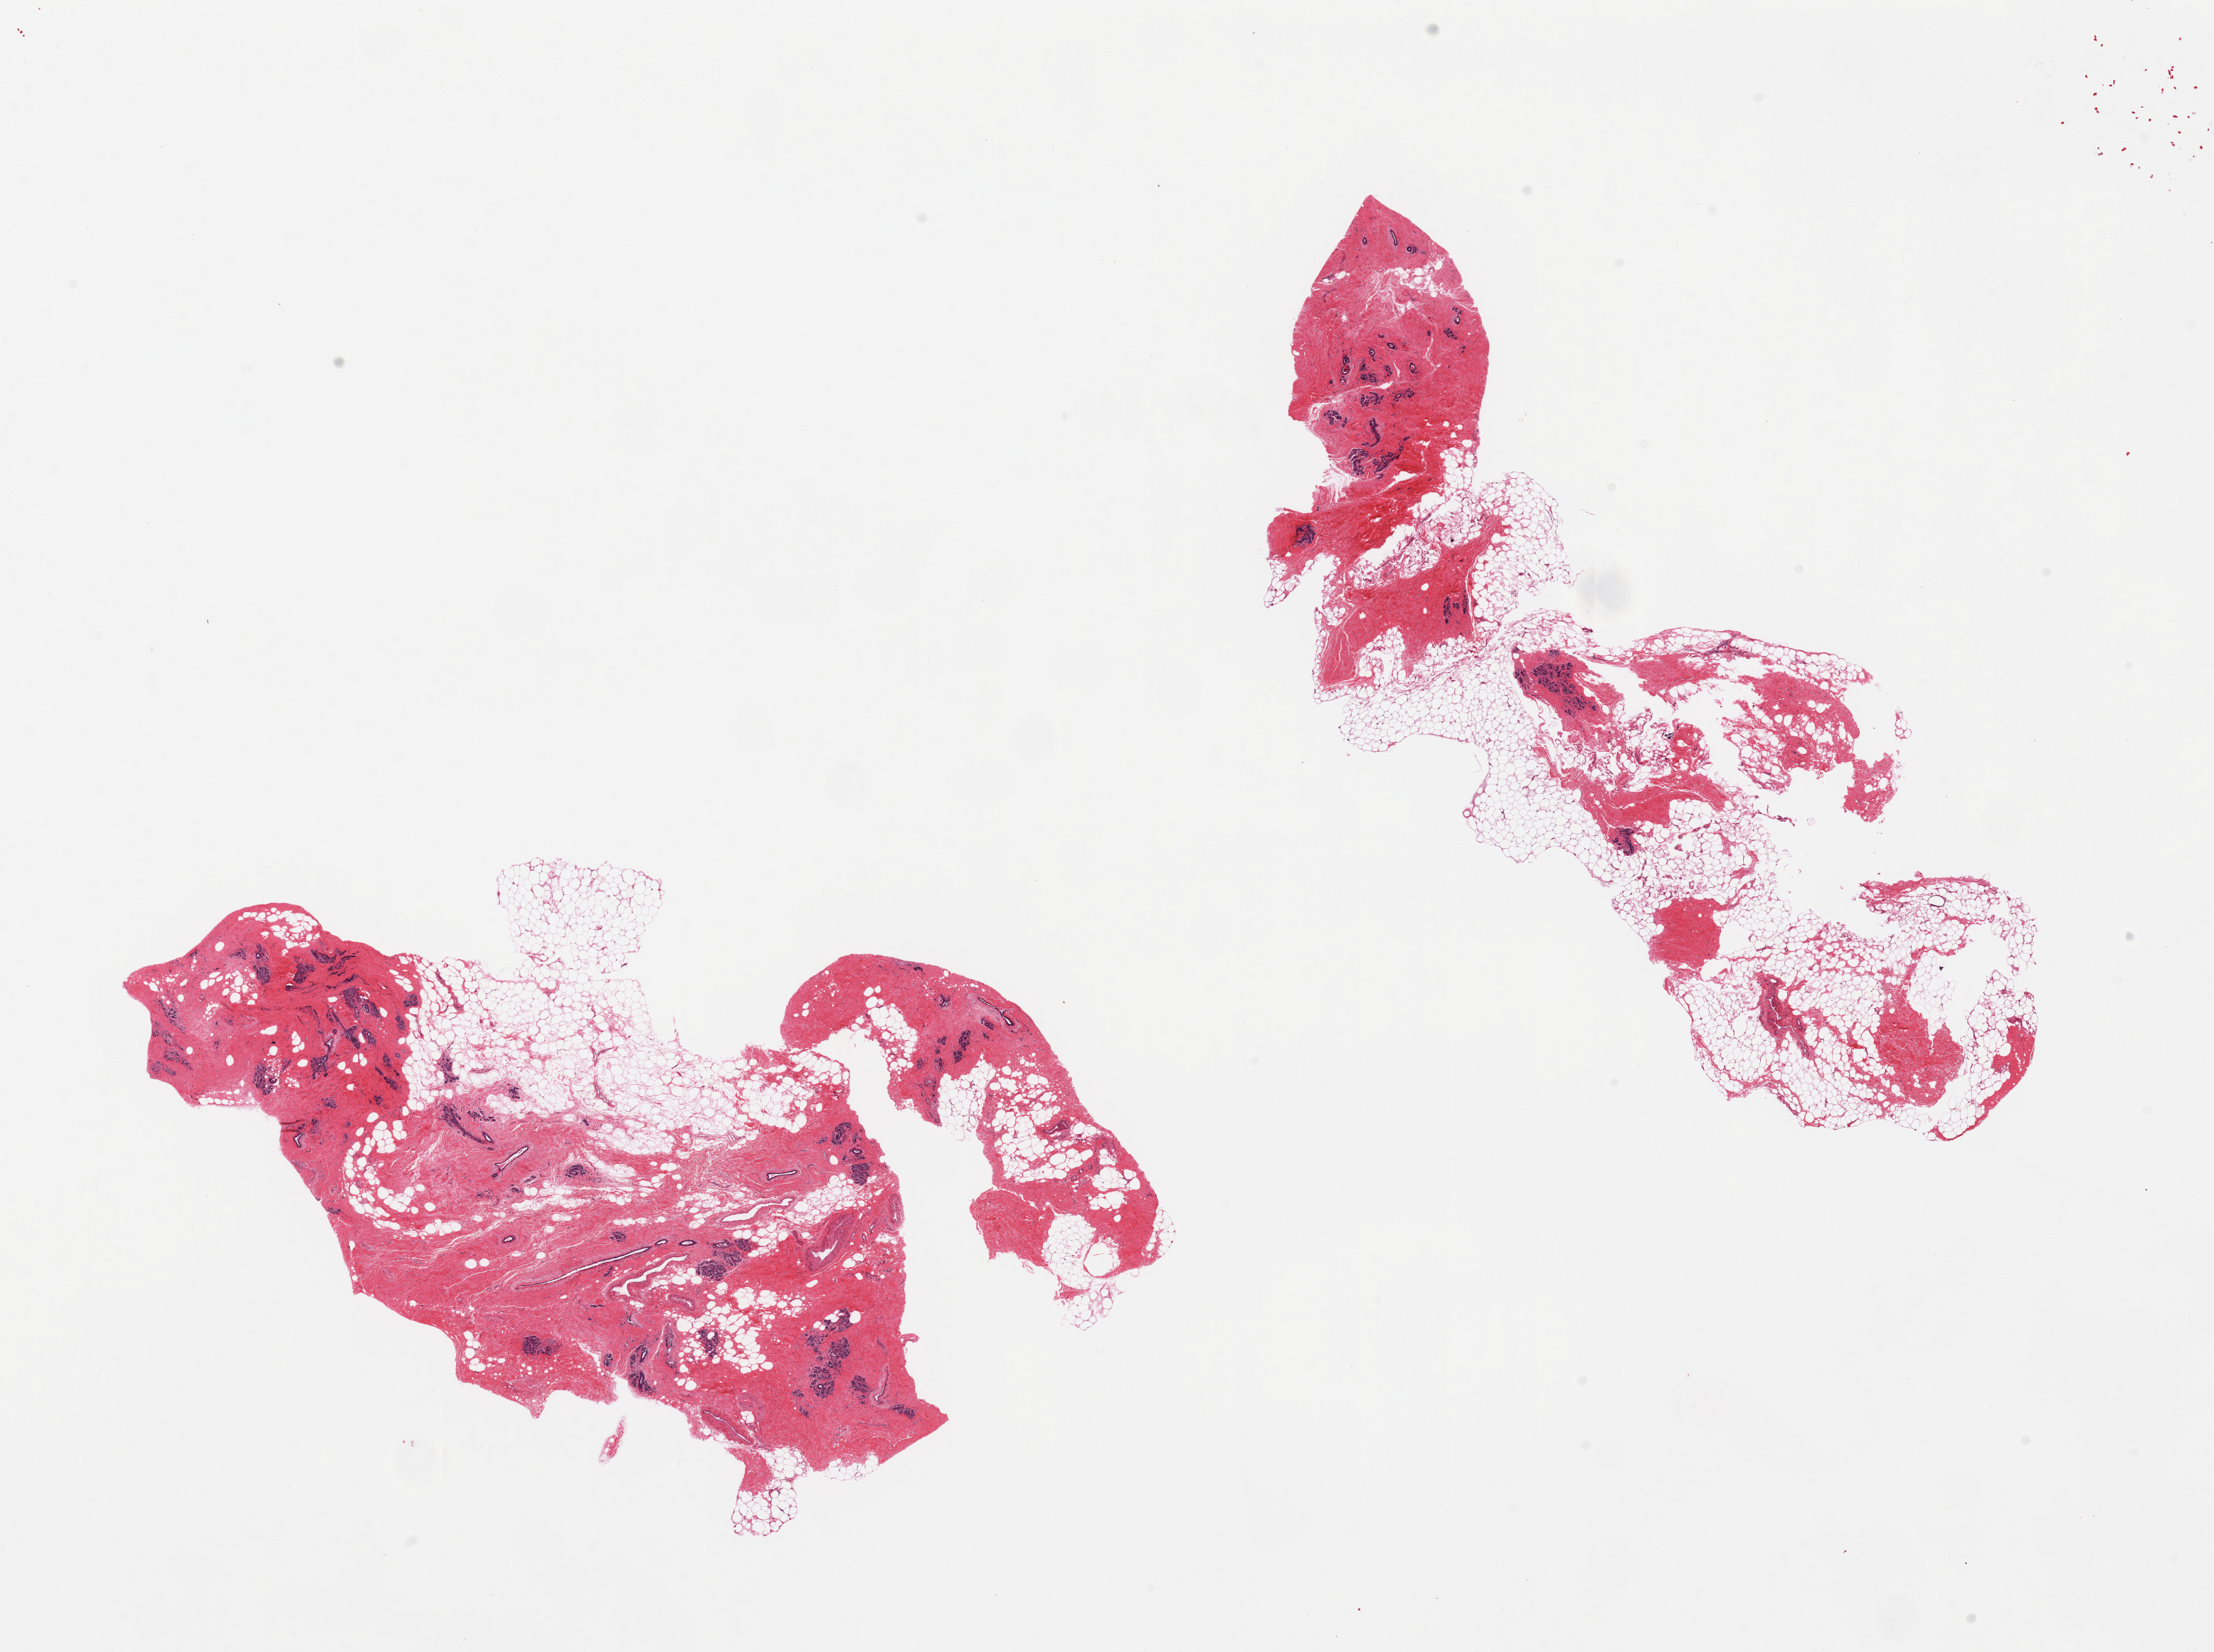
Haematoxylin and eosin whole-slide image, brightfield, low-resolution overview of the scanned area, about 24.6 x 18.4 mm, PAXgene-fixed, paraffin-embedded tissue, section of breast (target tissue), tissue donor sample.
* reviewer comment on this tissue sample: 2 pieces, 30% fat, 70% stroma, ductal and lobular units